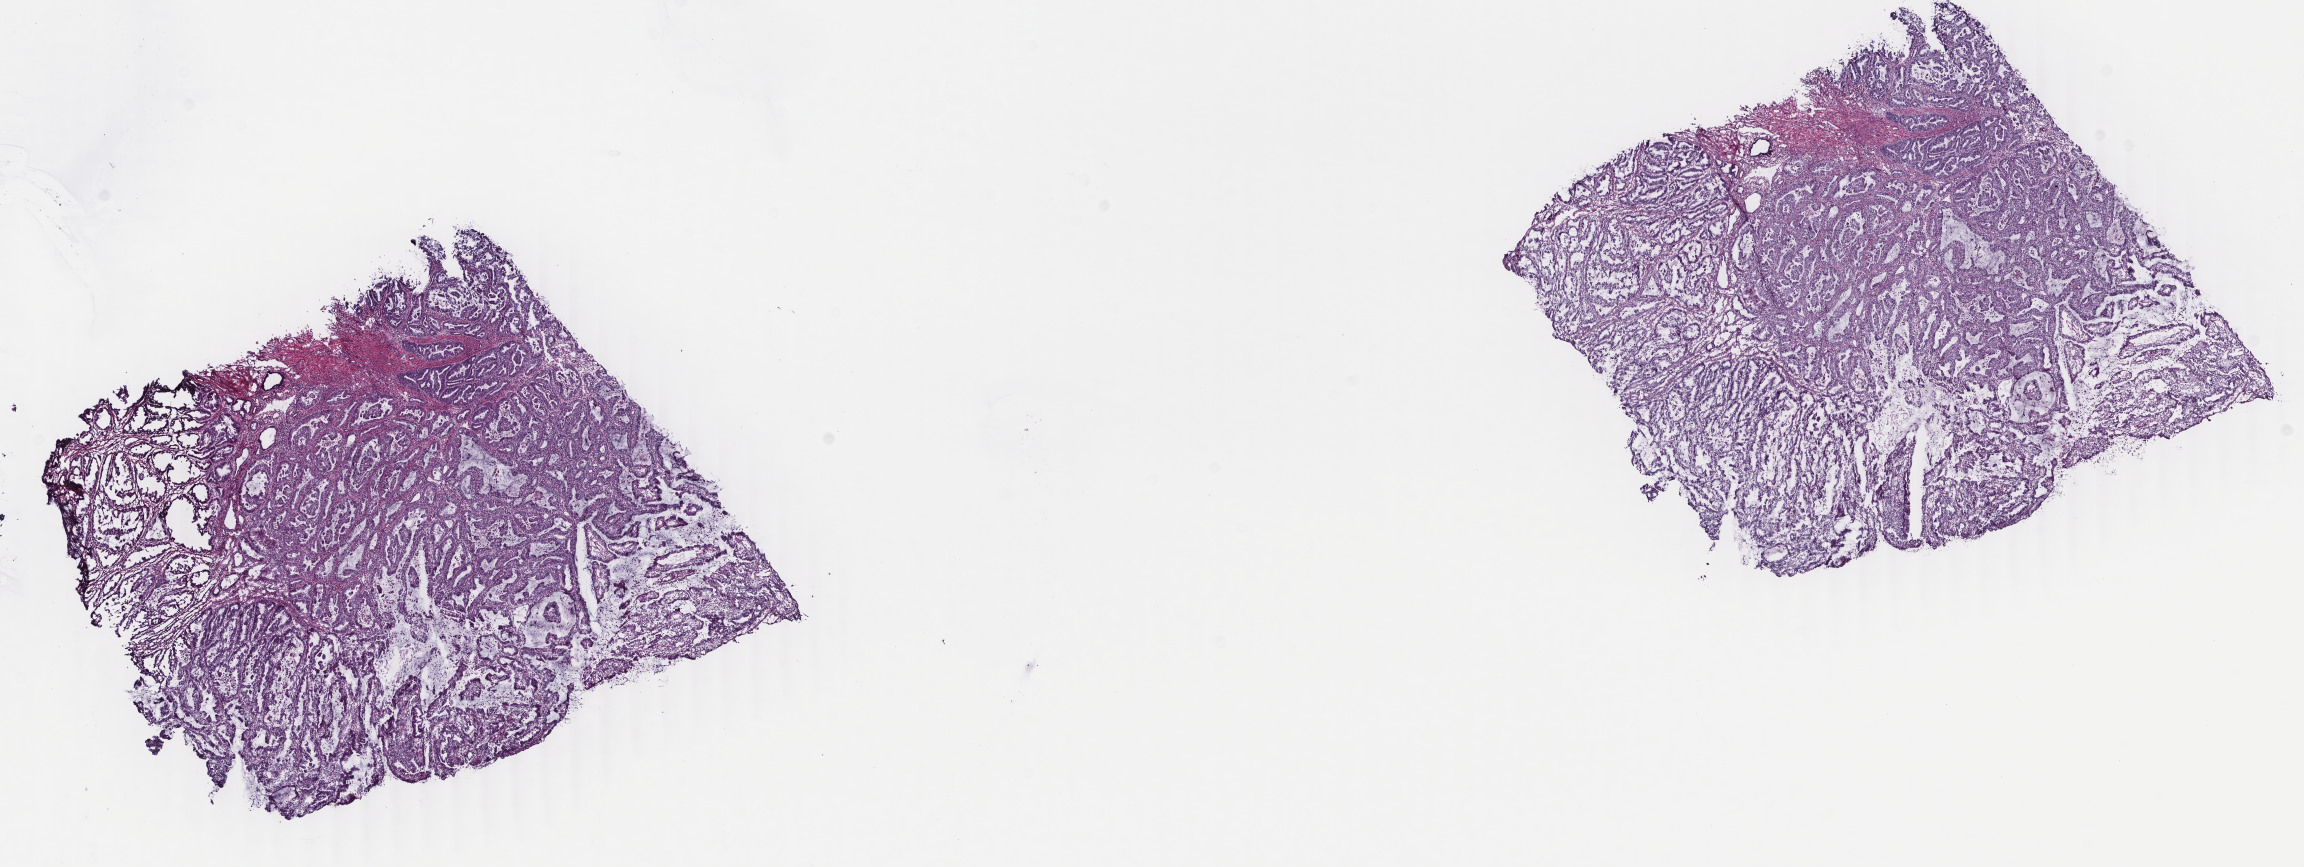
Digitized H&E tissue section (whole slide) — whole scanned area (about 18.3 x 6.9 mm) shown as a low-resolution overview; frozen section; primary tumour sample from the uterus. Female patient; age at initial diagnosis 49 years. Histologic grade: G2 (moderately differentiated). Pathologist review of this section (percent, as recorded): tumour cells 50%, tumour nuclei 60%, normal cells 0%, stromal cells 40%, necrosis 10%. Infiltration values recorded for this section: lymphocyte infiltration 5%, monocyte infiltration 8%, neutrophil infiltration 12%.
* lymph nodes positive (case pathology): 0 of 34 examined
* histologic diagnosis: Endometrioid adenocarcinoma, NOS
* FIGO stage: IC